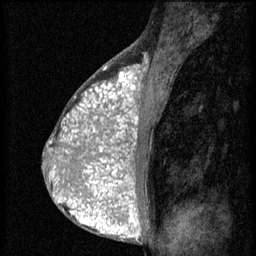
Breast MRI (dynamic contrast-enhanced), one sagittal slice; position 34 of 60 along the scan axis; 3 images stored at this slice position (order not interpretable as contrast timing); 1.5 T; TE 4.2 ms, TR 8.2 ms; 2 mm slice thickness; 256 × 256 image matrix. Female patient, age 38 years.
Structures marked on this image (semi-automatically segmented with operator editing):
- analysis volume of interest (the breast-tissue region the enhancement analysis was run in; not a lesion): bounding box (x1, y1, x2, y2) in pixels: (92, 112, 151, 171)
- tumour enhancement mask (voxels above the 70 % enhancement threshold inside the analysis volume of interest): (92, 112, 138, 171)